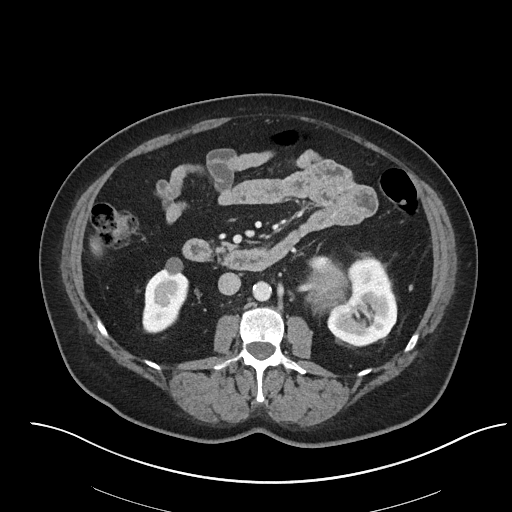
Contrast-enhanced abdominal CT, one axial slice. Reconstruction kernel I40f/2. 120 kVp. Intravenous contrast given. Soft-tissue window (W 400 / L 40 HU). 3 mm slice thickness. 512 × 512 image matrix, field of view 440 × 440 mm. Patient: female, 53 years. From the clinical record (not read from this slice): diagnosis: adrenocortical carcinoma; tumour side: left adrenal.
Annotated regions visible in this slice (semi-automatically segmented with operator editing):
- mass: box from (x=306, y=264) to (x=345, y=314) px